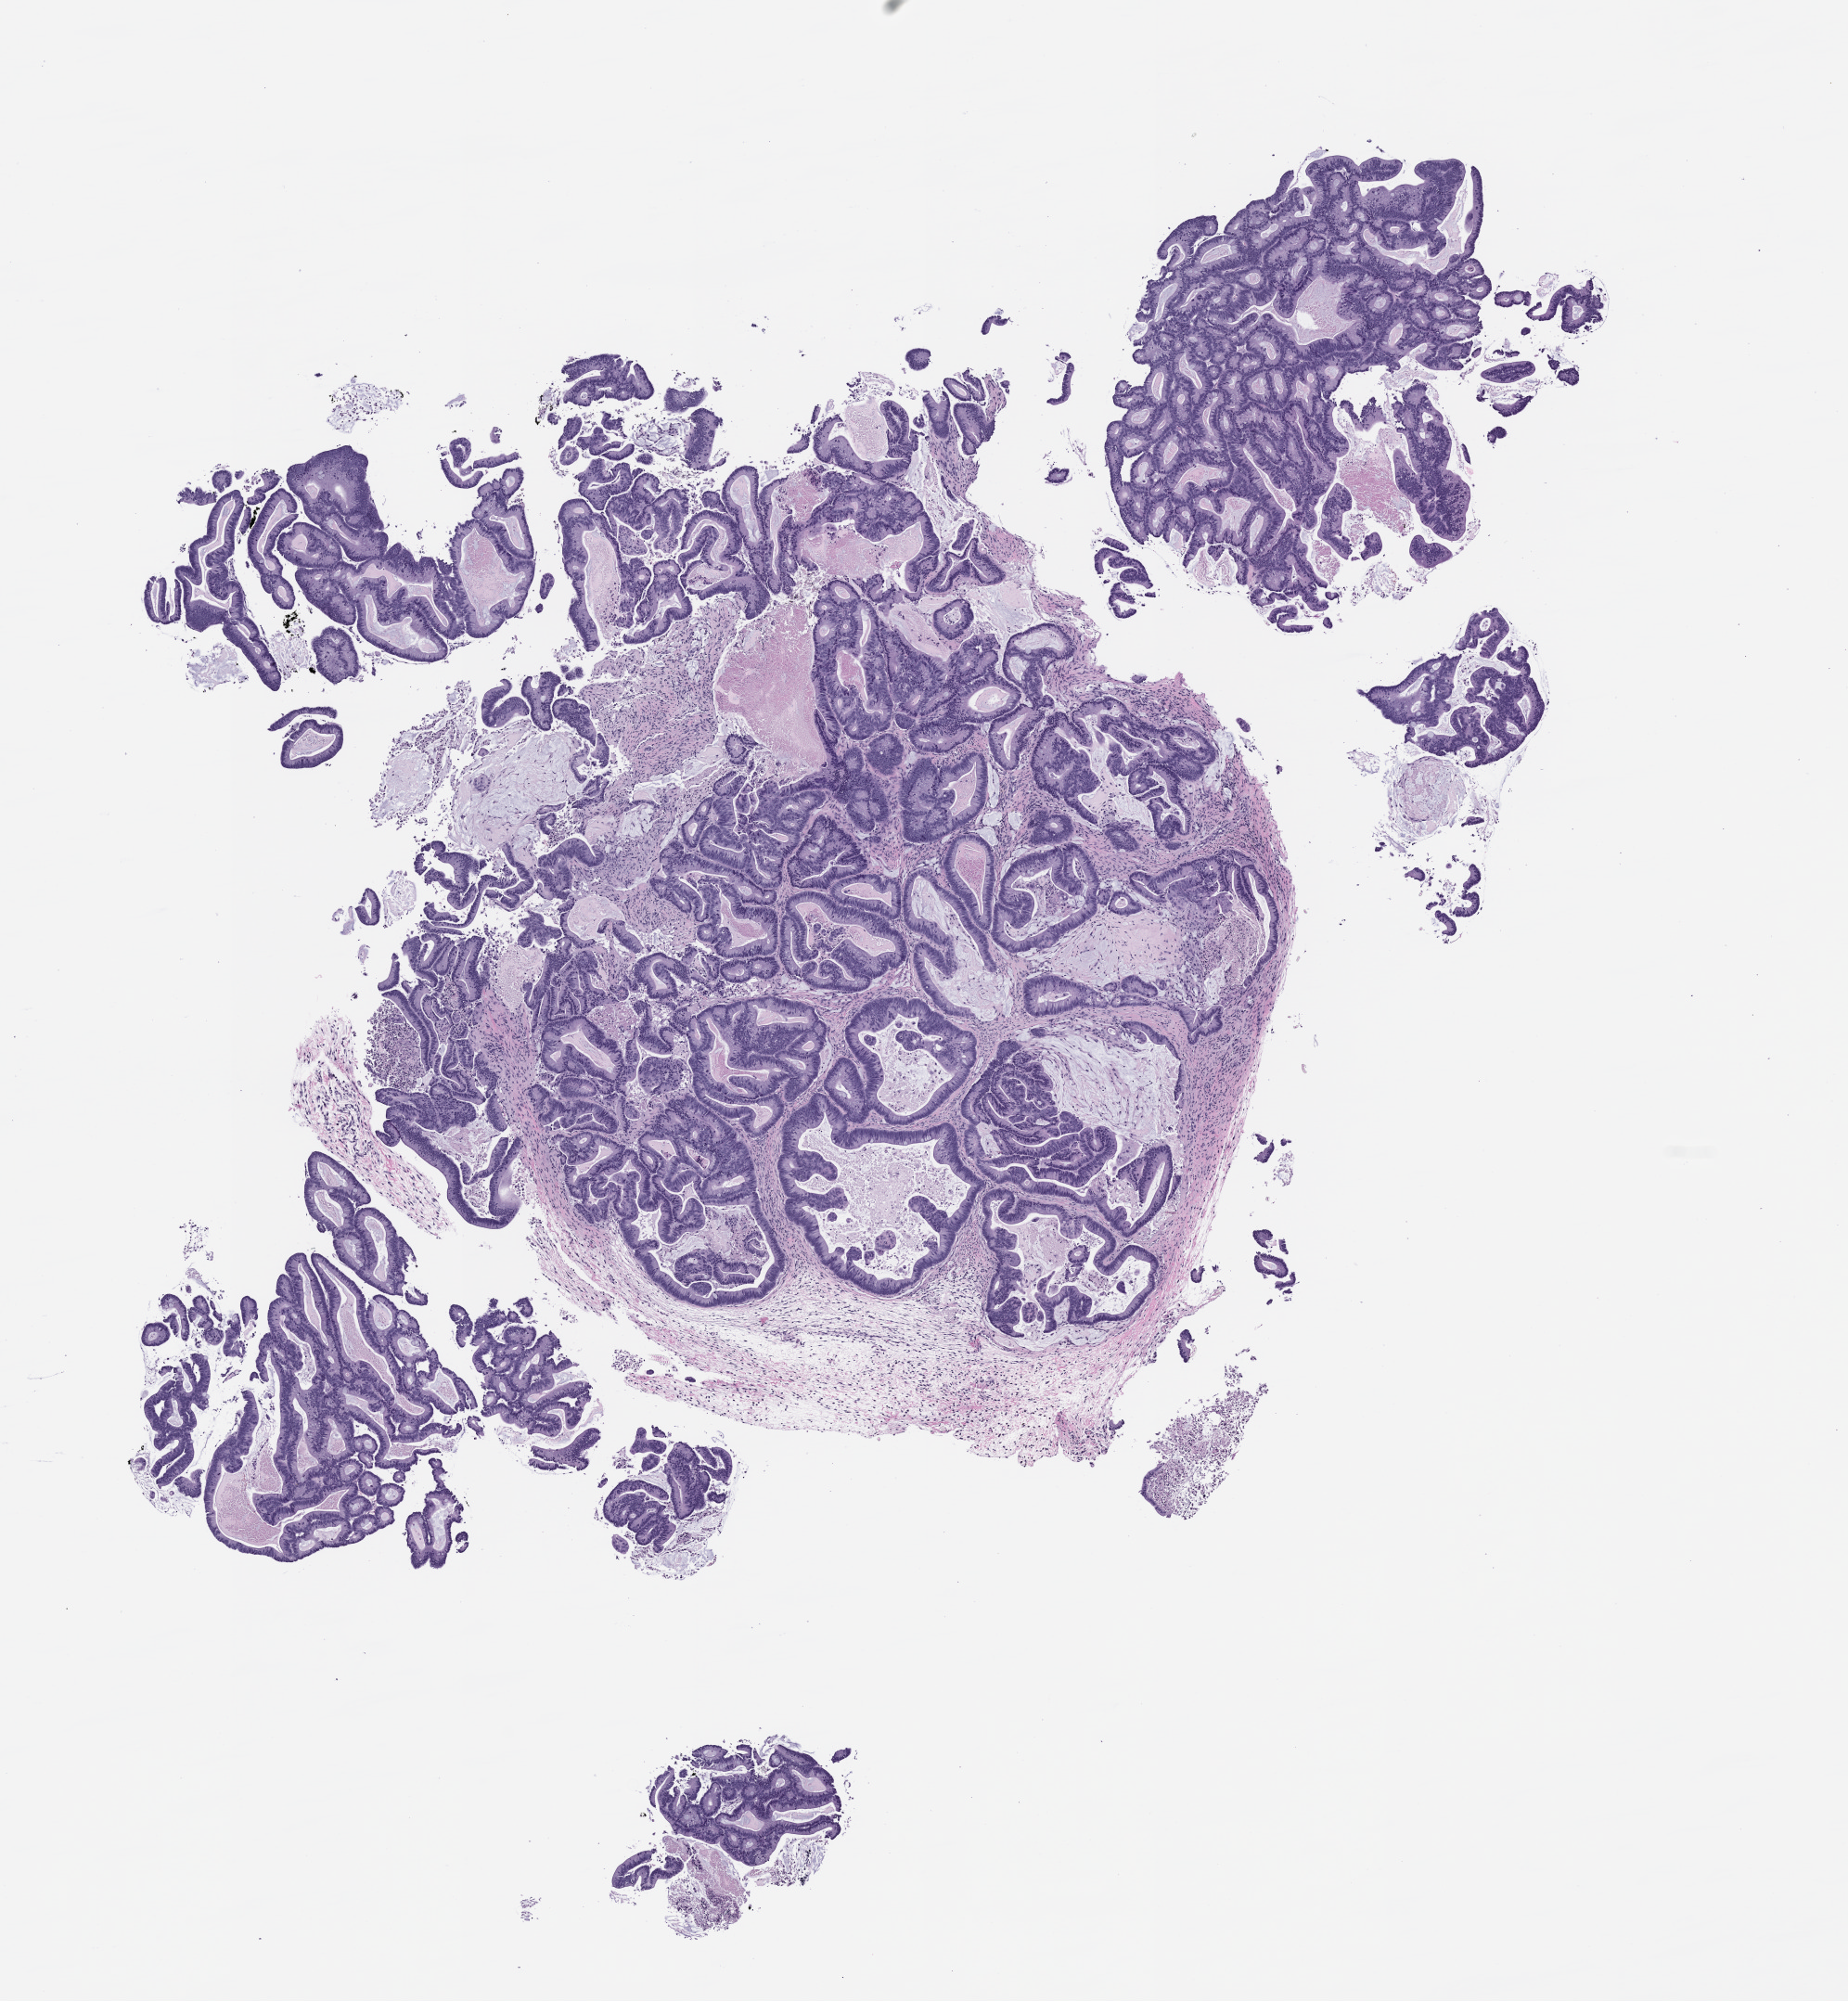
Whole-slide image, haematoxylin and eosin: patient-derived xenograft (human tumor grown in a mouse), passage 1 — whole scanned area (about 8.0 x 8.7 mm) shown as a low-resolution overview, formalin-fixed, paraffin-embedded (FFPE) tissue, tumor site category: colon.
Originating patient diagnosis: Colon Adenocarcinoma.